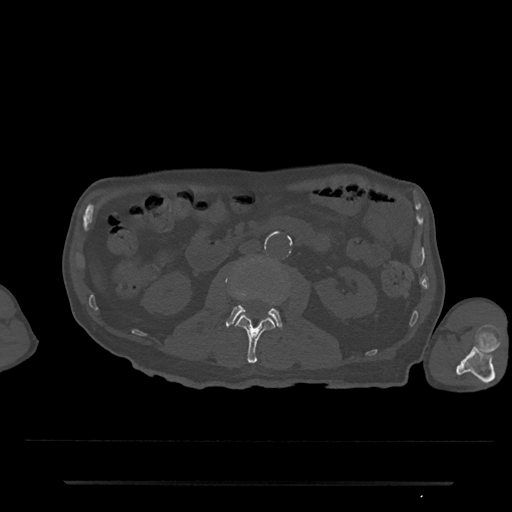
CT including the spine, one axial slice. Position 28 of 797 along the scan axis. Reconstruction kernel Br40s/3. 120 kVp. Bone window (W 1800 / L 400 HU). 512 × 512 image matrix, field of view 427 × 427 mm. Male patient, age 74 years. From the clinical record (not read from this slice): primary cancer: prostate.
Structures marked on this image (semi-automatically segmented with operator editing):
- L2 vertebra: box from (x=237, y=314) to (x=275, y=364) px
- L3 vertebra: (x=225, y=305)–(x=283, y=330)